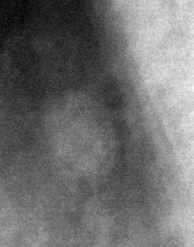
Cropped region of a digitized screen-film mammogram centred on a radiologist-marked abnormality, right breast, MLO view, BI-RADS breast density category 4 (scale 1–4).
Finding: mass, shape oval, margins circumscribed; BI-RADS assessment category 3; benign; no additional work-up was recommended (benign without callback).